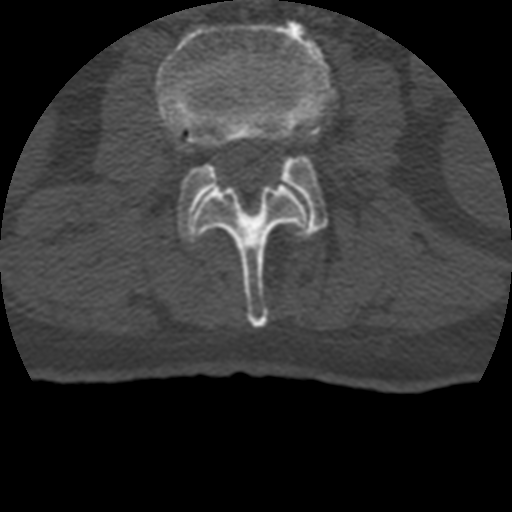
CT including the spine, one axial slice. Position 102 of 399 along the scan axis. 120 kVp. Bone window (W 1800 / L 400 HU). 1.25 mm slice thickness. 512 × 512 image matrix, field of view 160 × 160 mm. Patient age 69 years. Case-level facts recorded for this patient, not image findings: primary cancer: prostate.
Structures marked on this image (semi-automatically segmented with operator editing):
- L2 vertebra: bounding box (x1, y1, x2, y2) in pixels: (193, 185, 309, 328)
- L3 vertebra: (155, 20, 335, 237)